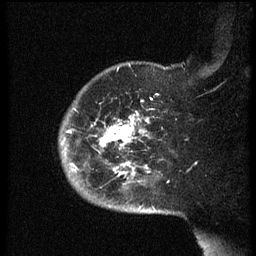
Breast MRI (dynamic contrast-enhanced), one sagittal slice. Position 49 of 60 along the scan axis. Dynamic contrast-enhanced series, image 2 of 3 at this slice position (ordered by acquisition). 1.5 T. TE 4.2 ms, TR 8.4 ms. 256 × 256 image matrix. Female patient, age 38 years. From the clinical record (not read from this slice): setting: breast cancer imaged before/during neoadjuvant chemotherapy; receptor status: HER2-positive.
Annotated regions visible in this slice (semi-automatically segmented with operator editing):
- analysis volume of interest (the breast-tissue region the enhancement analysis was run in; not a lesion): box from (x=60, y=74) to (x=167, y=202) px
- tumour enhancement mask (voxels above the 70 % enhancement threshold inside the analysis volume of interest): (x=63, y=109)–(x=151, y=186)